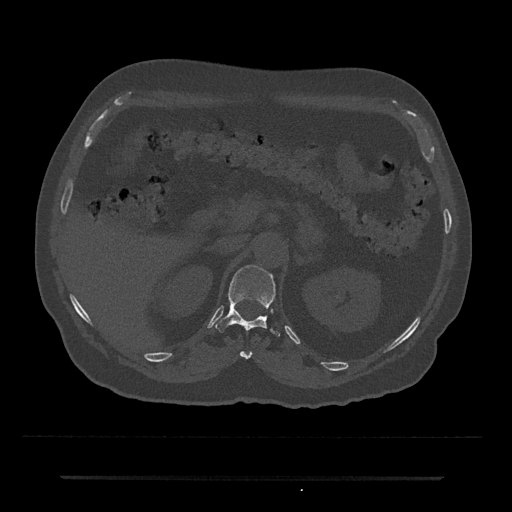
CT including the spine, one axial slice. Slice 130 of 797 in the series (ordered by position). 120 kVp. Bone window (W 1800 / L 400 HU). 0.5 mm slice thickness. 512 × 512 image matrix. Male patient, age 69 years. From the clinical record (not read from this slice): primary cancer: prostate.
Outlined on this slice (semi-automatically segmented with operator editing):
- T11 vertebra: bounding box [x1, y1, x2, y2] px = [240, 351, 252, 360]
- T12 vertebra: [215, 265, 280, 336]